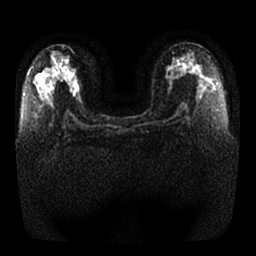
Breast MRI, one axial slice; position 13 of 25 along the scan axis; diffusion-weighted series; image 2 of 4 stored at this slice position (different b-values; order by instance number); 1.5 T; 4 mm slice thickness; 256 × 256 image matrix, field of view 350 × 350 mm. Female patient.
Structures marked on this image (outlined manually by an expert reader):
- tumour on diffusion-weighted imaging: box from (x=71, y=78) to (x=79, y=92) px